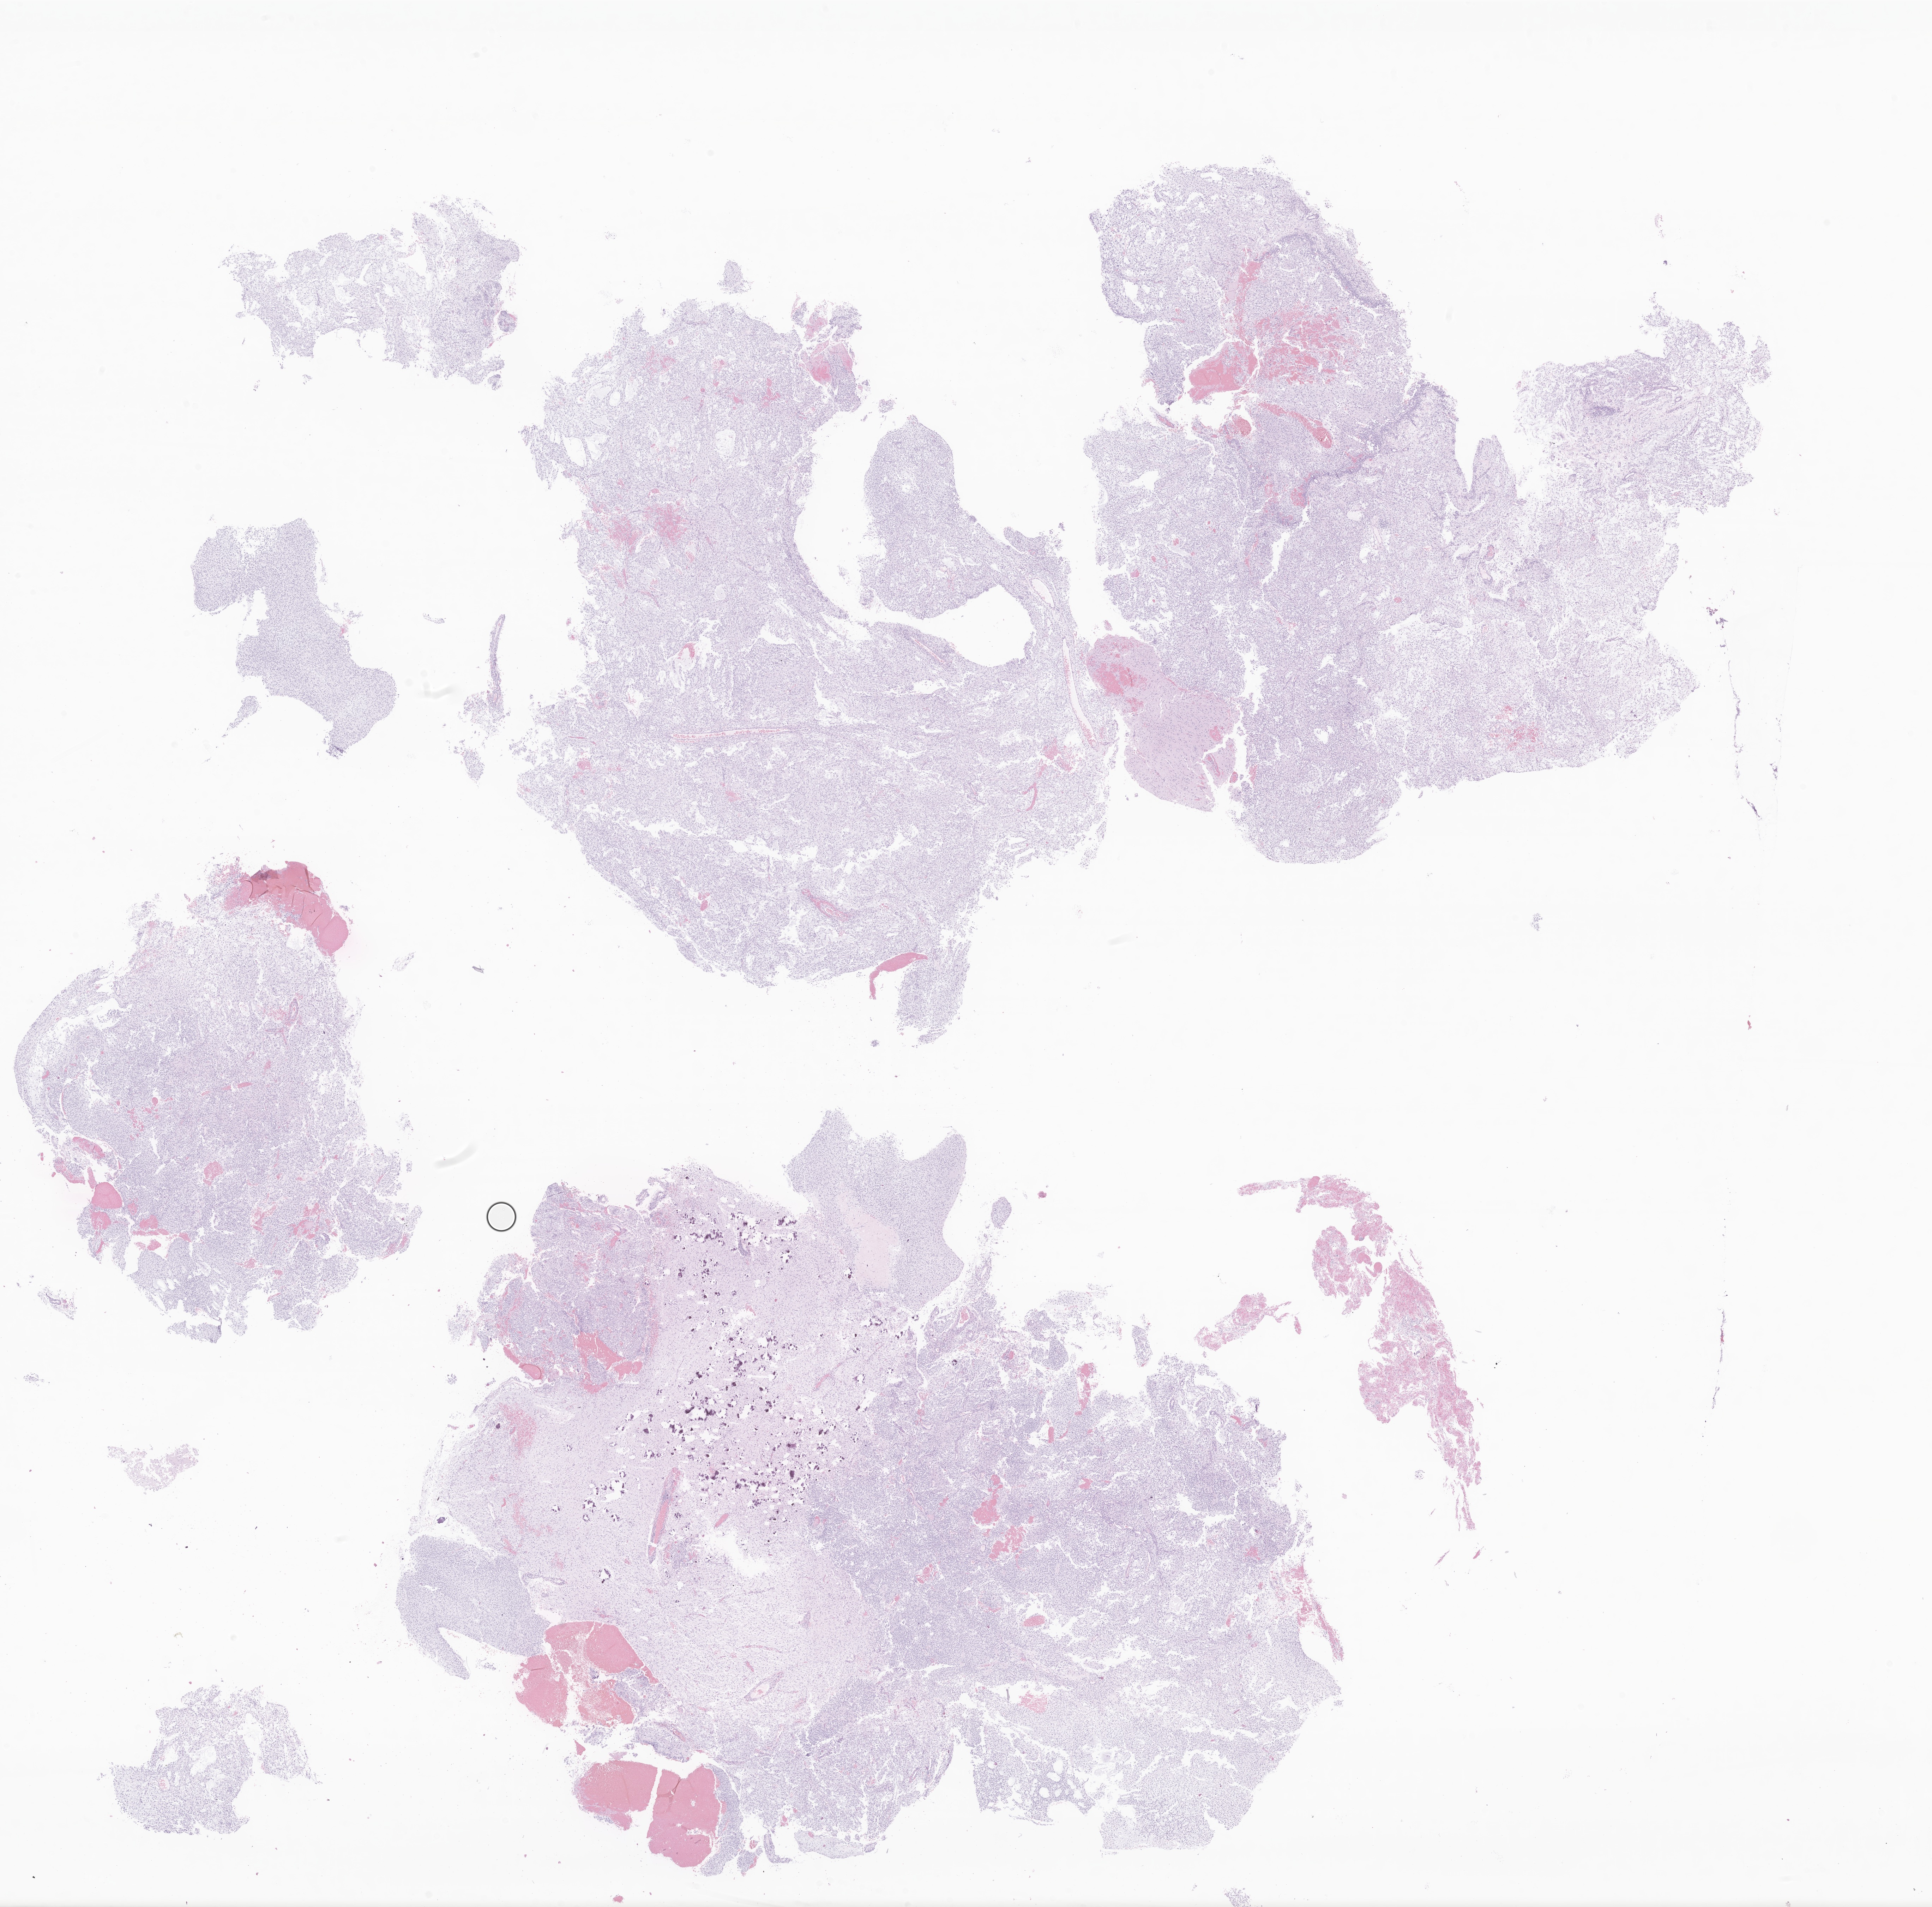
Haematoxylin and eosin whole-slide image of tumor tissue from the occipital lobe — low-resolution overview of the scanned area, about 23.1 x 22.8 mm; formalin-fixed, paraffin-embedded (FFPE) tissue. Female patient, age 134 months.
Recorded diagnosis: Tumor cells, malignant.